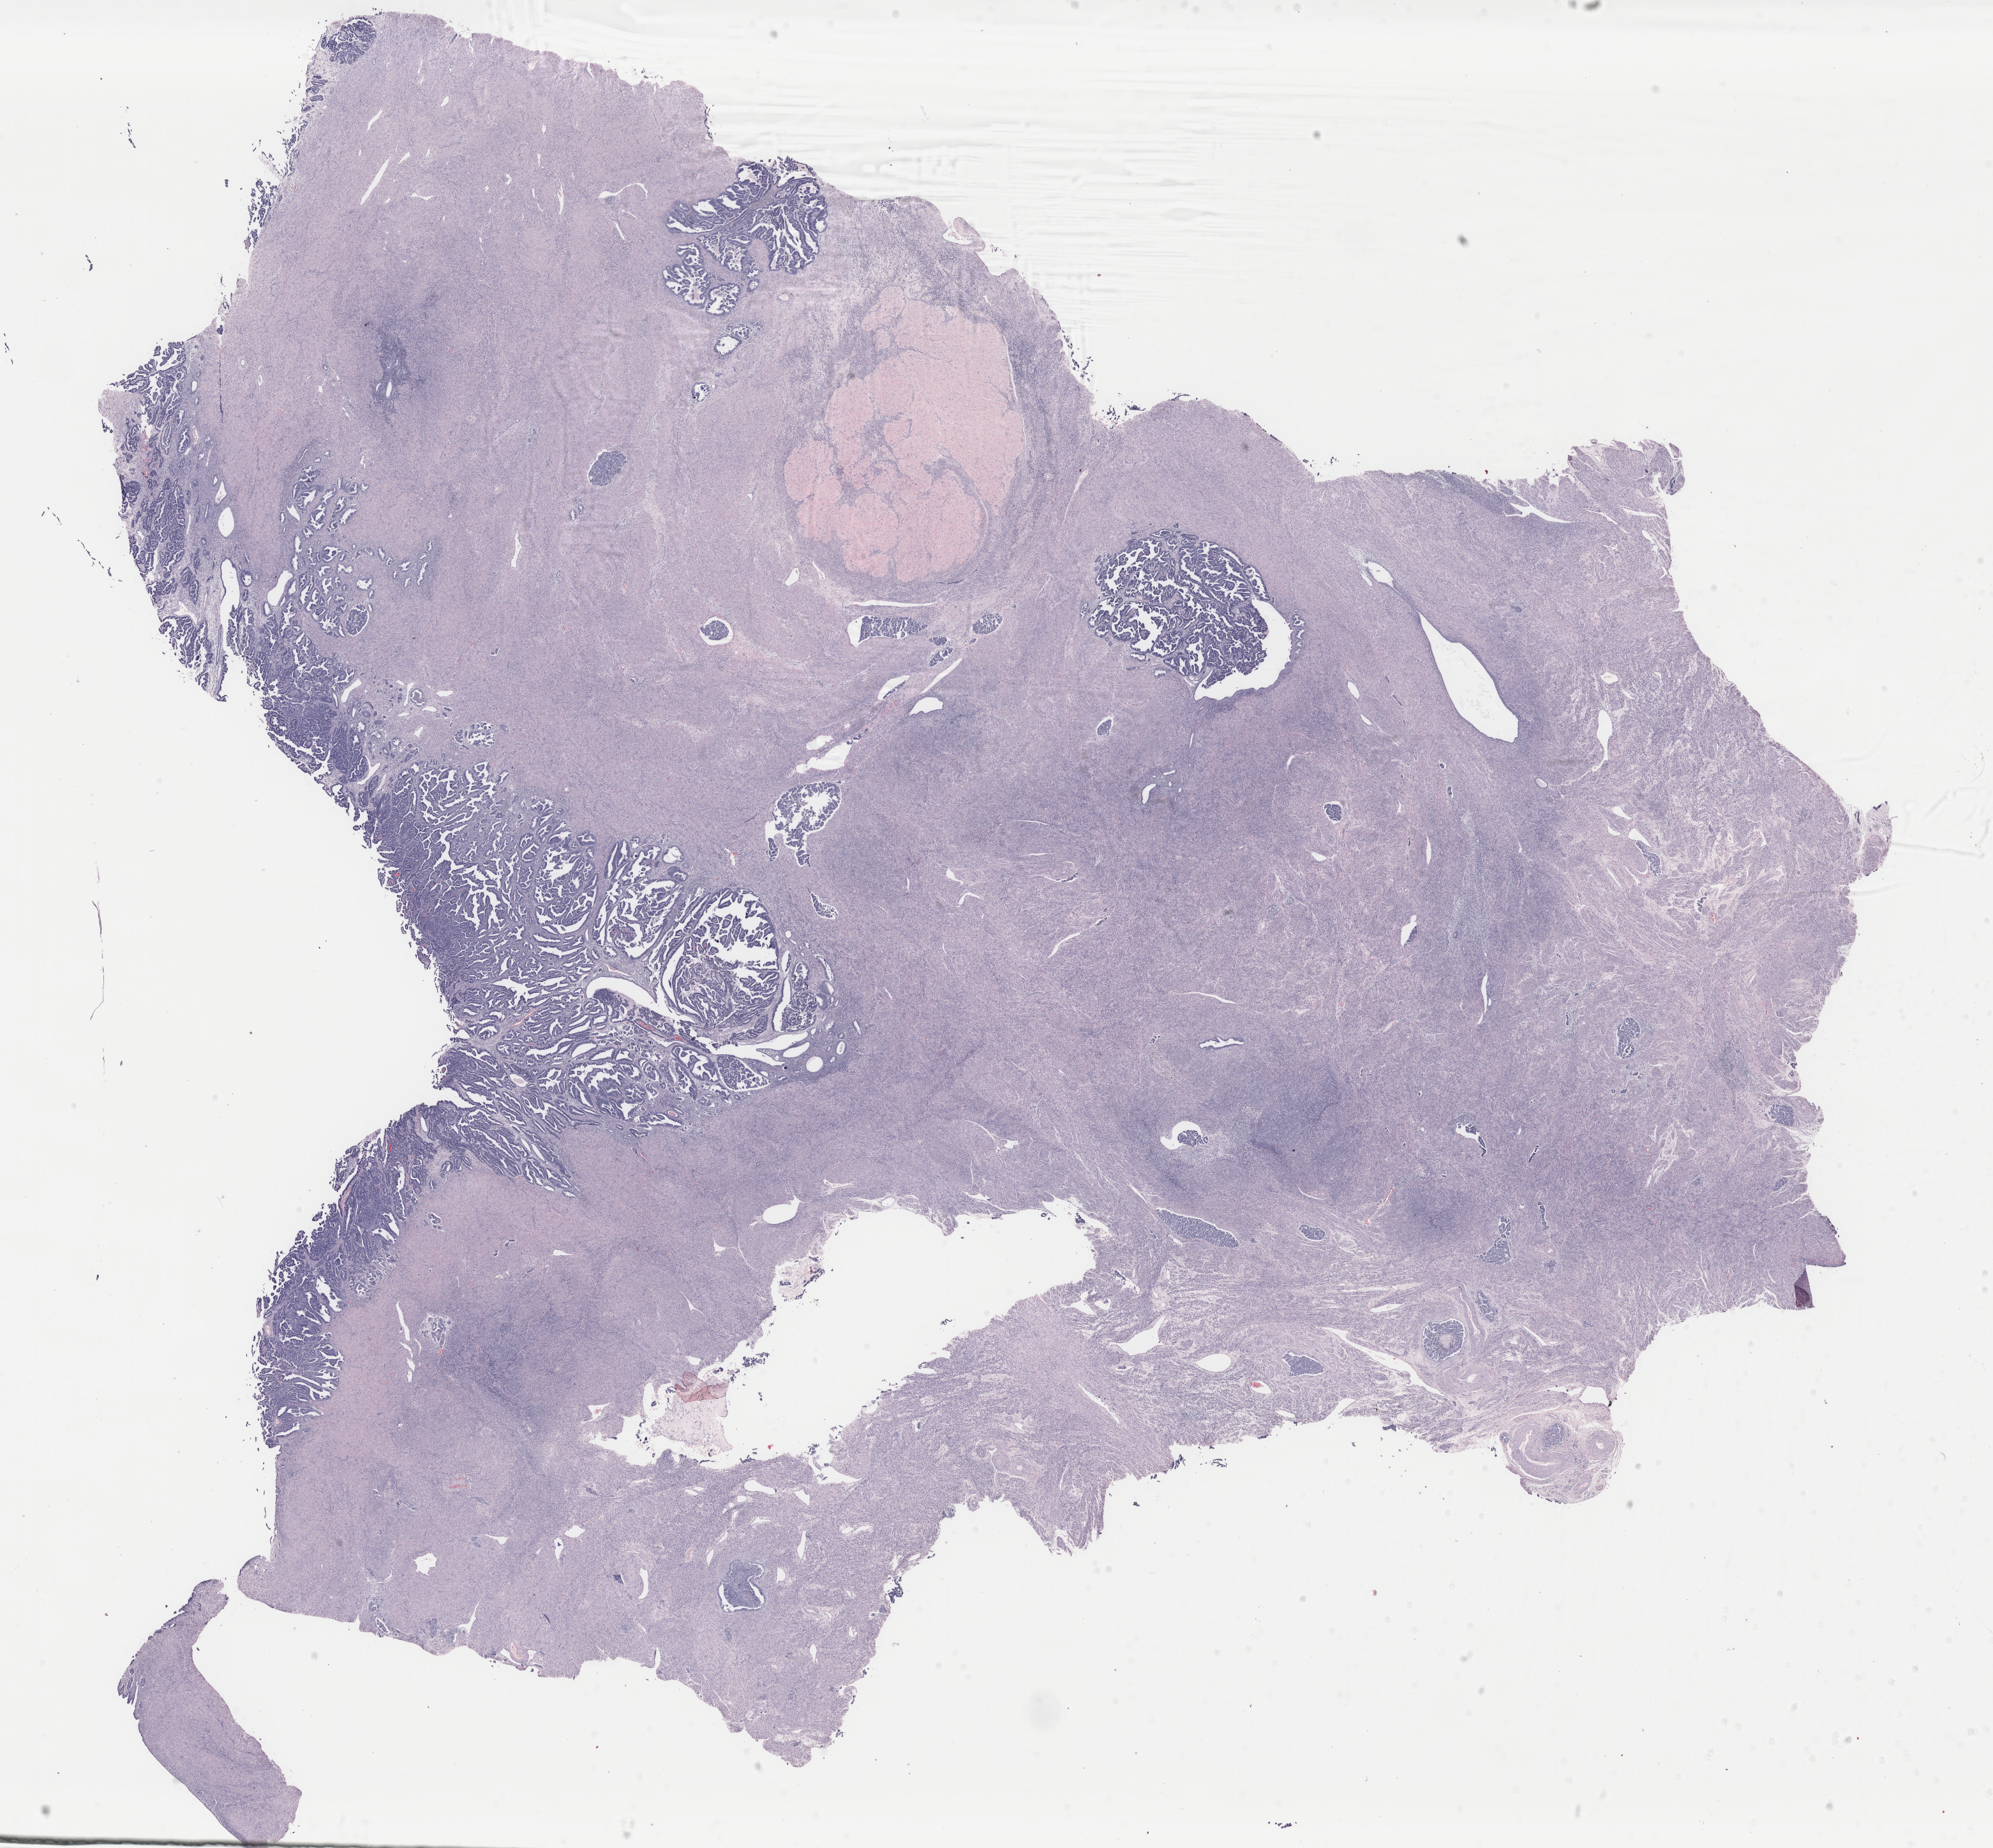
Digitized H&E-stained tissue section (whole slide), low-resolution overview of the scanned area, about 24.8 x 23.0 mm (slide scanned at 40x), formalin-fixed paraffin-embedded (FFPE) diagnostic section, primary tumour sample from the uterus. Female patient; age at initial diagnosis 67 years.
Diagnosis: Mullerian mixed tumor. FIGO stage: IIIC2.